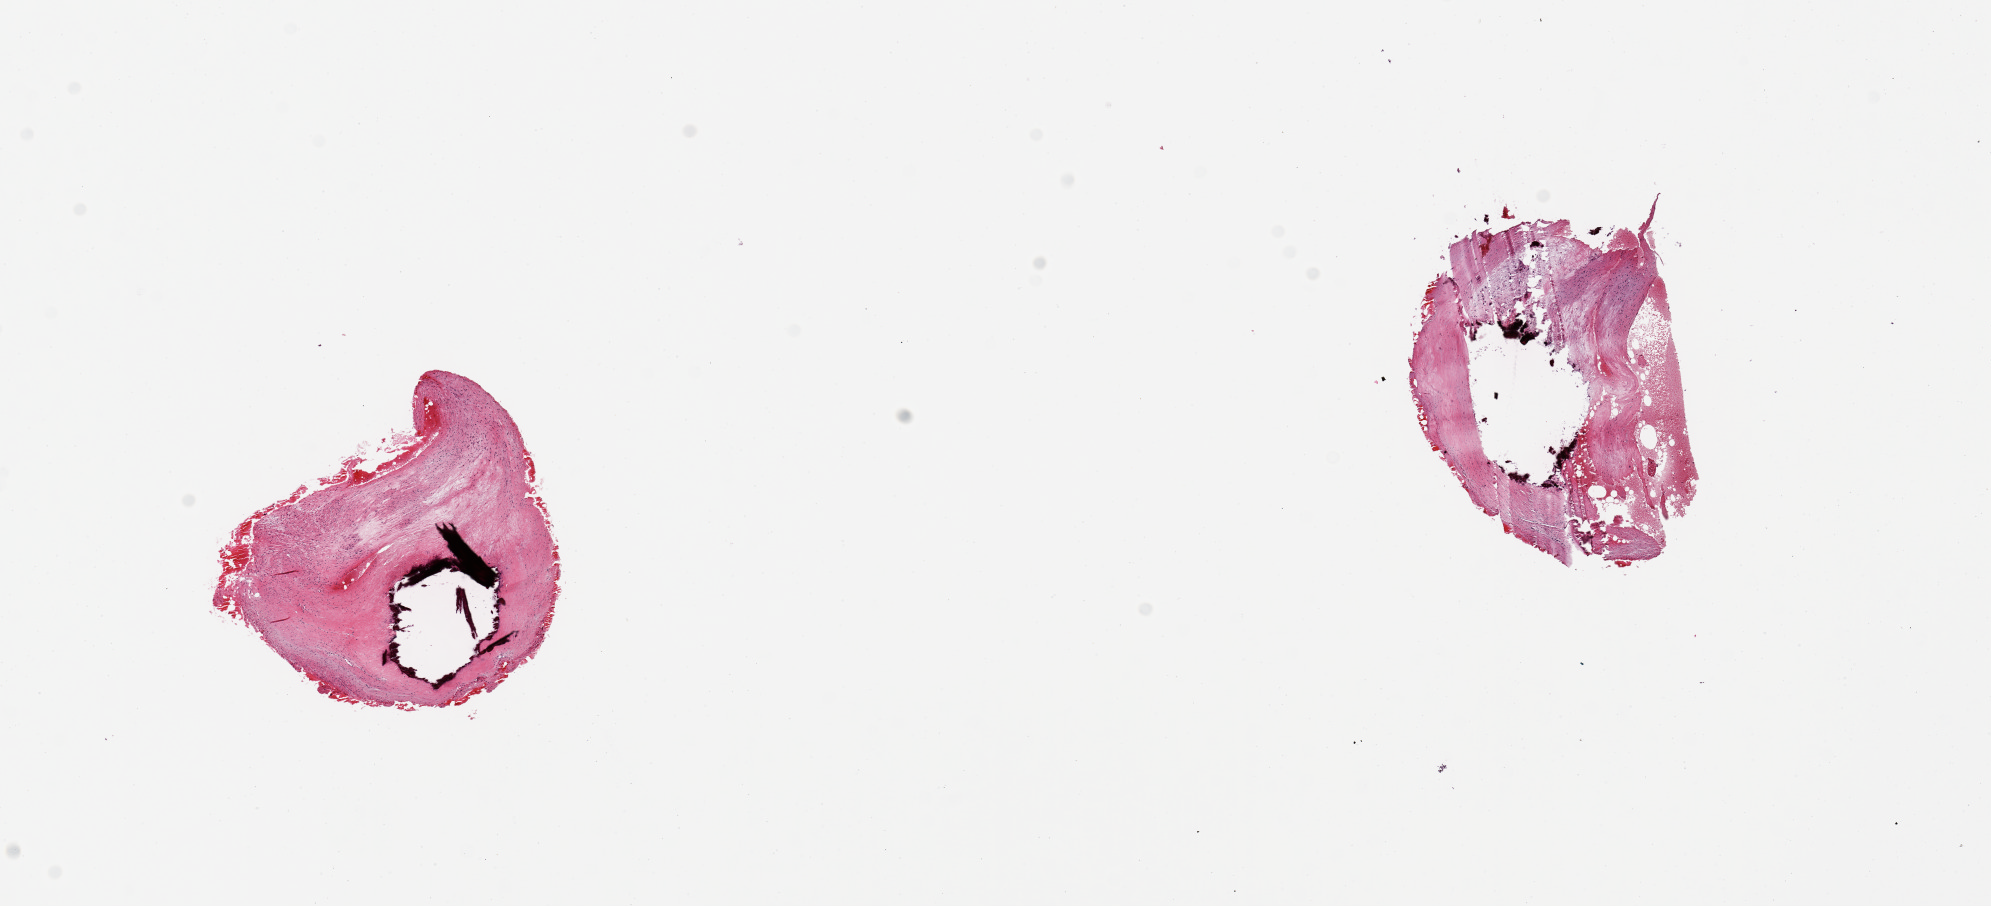
Digitized haematoxylin and eosin-stained section, shown as a low-resolution overview of the whole scanned area (about 15.8 x 7.2 mm); PAXgene-fixed, paraffin-embedded tissue; target tissue: coronary artery; tissue donor sample. Donor sex: female.
* review note (as recorded): 2 pieces, 3x2 & 3x2mm; subtotally occlusive, calcifying atherosclerosis; One aliquot has ~1mm adherent fatty nubbin